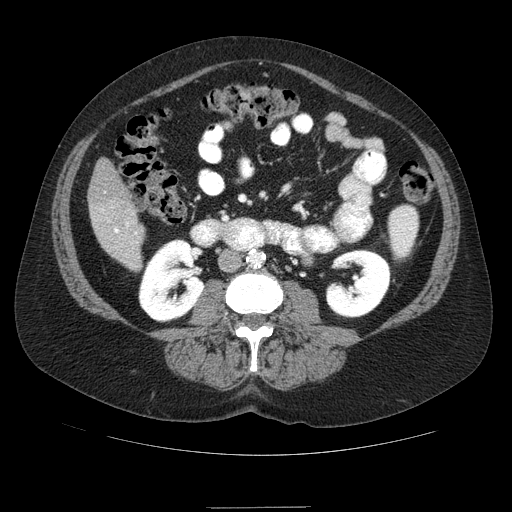
Contrast-enhanced abdominal CT (liver protocol), one axial slice. Position 19 of 89 along the scan axis. Soft-tissue window (W 400 / L 40 HU). 2.5 mm slice thickness. 512 × 512 image matrix, field of view 400 × 400 mm. From the clinical record (not read from this slice): diagnosis: hepatocellular carcinoma (patient treated with transarterial chemoembolisation; whether this scan precedes or follows treatment is not stated here); TNM stage (as recorded): Stage-IIIB; Child-Pugh class: A.
Annotated regions visible in this slice (semi-automatically segmented with operator editing):
- liver parenchyma outside the tumour (the mass and vessels are separate outlines, so this box may not span the whole liver): bounding box <88,158,144,270> (left, top, right, bottom; pixels)
- liver vessels: <114,222,136,235>